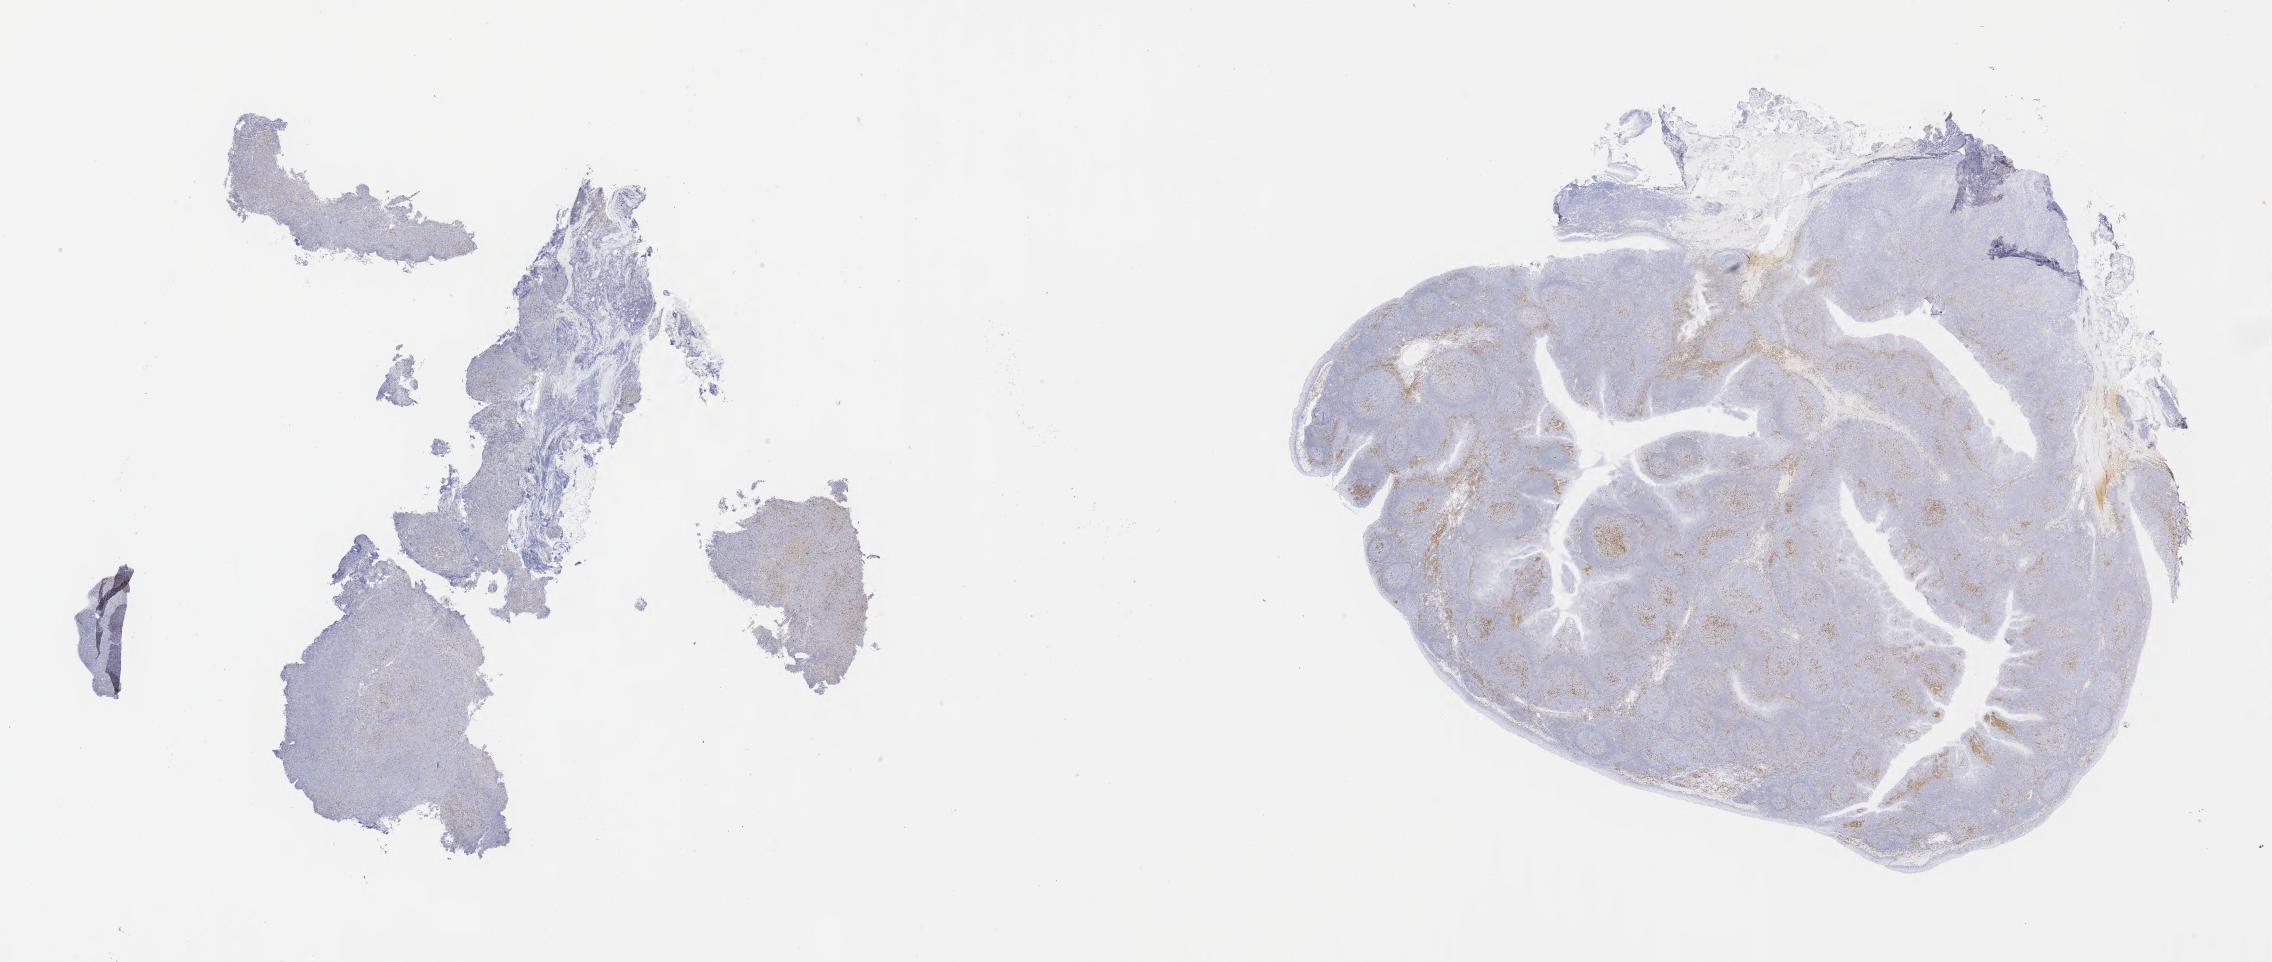
Whole-slide image, immunohistochemical stain for IRF4/MUM1 — shown as a low-resolution overview of the whole scanned area (about 36.7 x 15.5 mm), tumor tissue, anatomic site: liver. Patient: female, age 36 years.
* histologic diagnosis: Diffuse large B-cell lymphoma, NOS